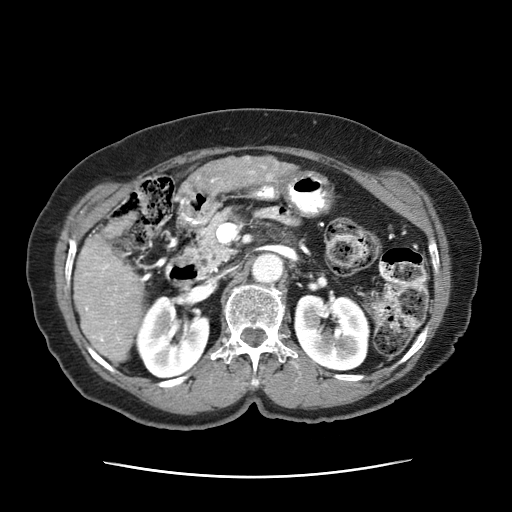
Contrast-enhanced abdominal CT (liver protocol), one axial slice. Slice 19 of 63 in the series (ordered by position). Reconstruction kernel STANDARD. 120 kVp. Intravenous contrast given. Soft-tissue window (W 400 / L 40 HU). 2.5 mm slice thickness. 512 × 512 image matrix, field of view 360 × 360 mm. Female patient, age 79 years. From the clinical record (not read from this slice): diagnosis: hepatocellular carcinoma (patient treated with transarterial chemoembolisation; whether this scan precedes or follows treatment is not stated here); TNM stage (as recorded): Stage-II; Child-Pugh class: B; tumour differentiation: well differentiated.
Annotated regions visible in this slice (semi-automatically segmented with operator editing):
- abdominal aorta: bounding box [x1, y1, x2, y2] px = [252, 251, 284, 282]
- liver parenchyma outside the tumour (the mass and vessels are separate outlines, so this box may not span the whole liver): [73, 232, 149, 366]
- mass: [180, 155, 295, 192]
- liver vessels: [85, 264, 131, 344]